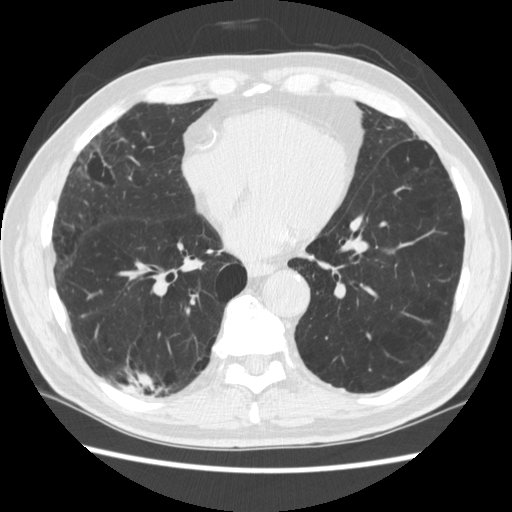
Low-dose screening chest CT, axial slice; third annual screen; lung window (W 1500 / L -600 HU); 1.25 mm slice thickness; standard (soft-tissue) reconstruction kernel (STANDARD); slice 157 of 266 in the series; 512 × 512 image matrix, field of view 360 × 360 mm. Male, age 70 years at enrolment. Former smoker at enrolment.
Expert-annotated lung lesion, bounding box <128,359,179,415> (left, top, right, bottom; pixels). The screening reader recorded 4 non-calcified nodules or masses ≥4 mm on this exam (right lower lobe, right lower lobe, left lower lobe, left lower lobe); which of them this box marks is not recorded. Official screen result: positive, other. Later outcome: lung cancer diagnosed 253 days after this screen — squamous cell carcinoma, NOS, right upper lobe, poorly differentiated (G3), stage IV (AJCC 6th edition).